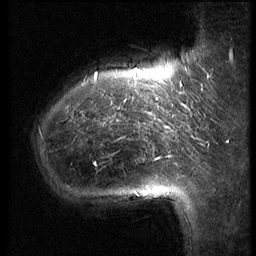
Breast MRI (dynamic contrast-enhanced), one sagittal slice; 3 images stored at this slice position (order not interpretable as contrast timing); 1.5 T; TE 4.2 ms, TR 9 ms; 2.5 mm slice thickness; 256 × 256 image matrix, field of view 180 × 180 mm. Female patient, age 39 years. From the clinical record (not read from this slice): setting: breast cancer imaged before/during neoadjuvant chemotherapy; receptor status: HER2-positive.
Structures marked on this image (semi-automatic segmentation, software-assisted and operator-edited):
- analysis volume of interest (the breast-tissue region the enhancement analysis was run in; not a lesion): bounding box [x1, y1, x2, y2] px = [28, 64, 171, 221]
- tumour enhancement mask (voxels above the 140 % enhancement threshold inside the analysis volume of interest): [97, 72, 169, 163]